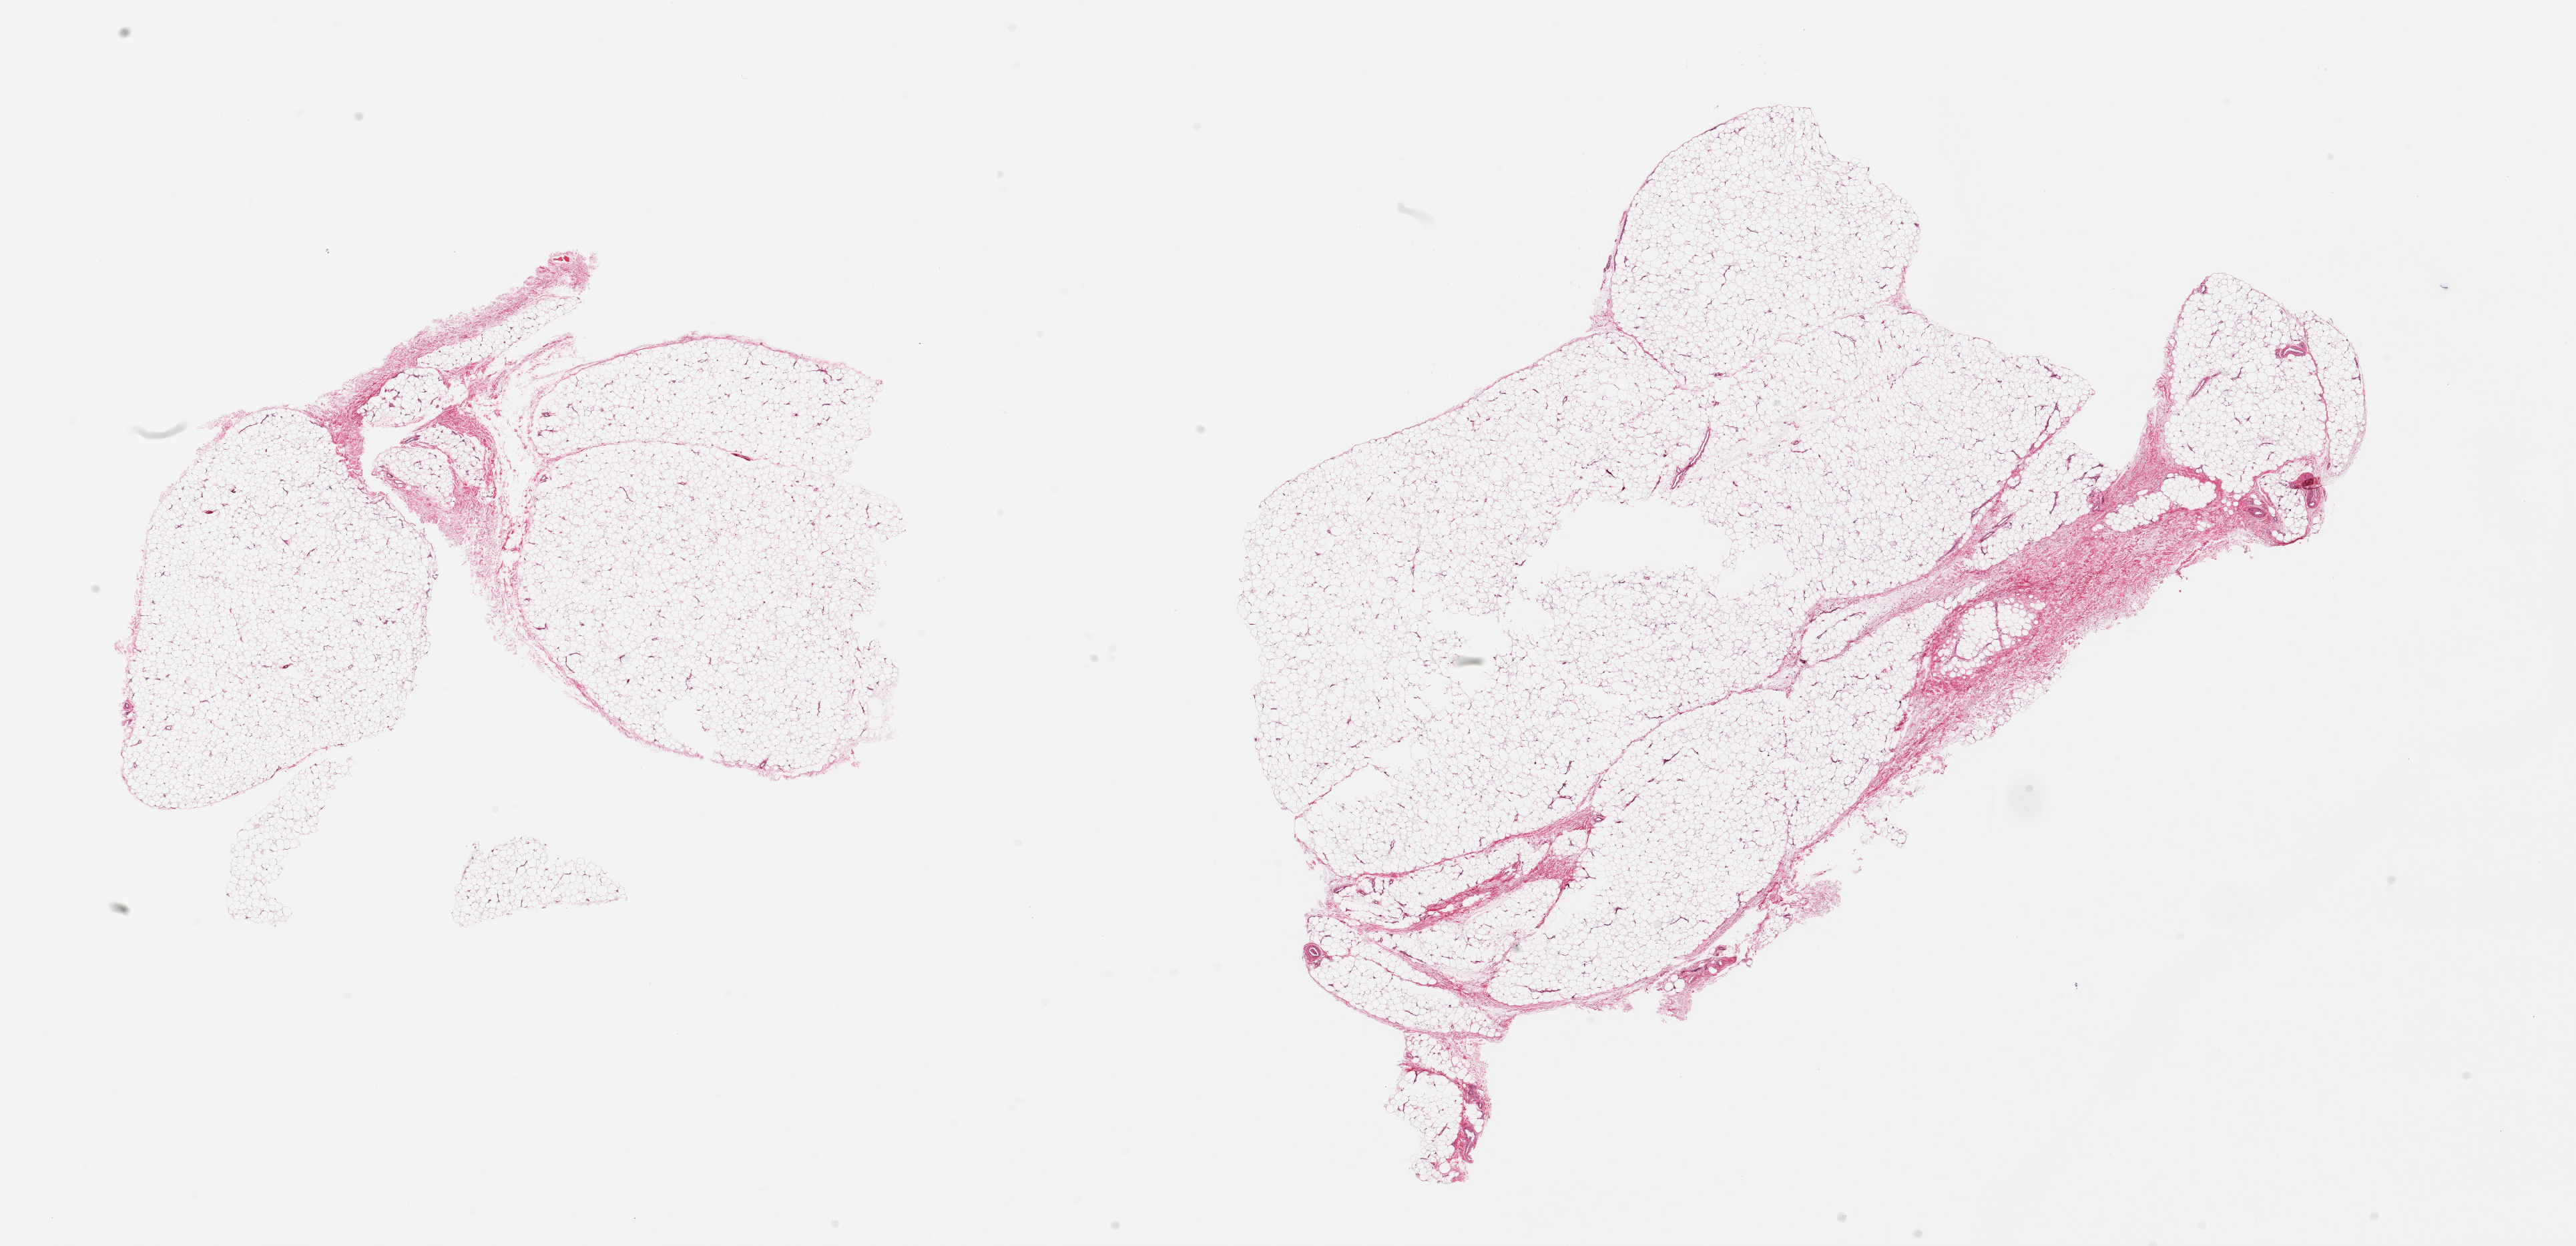
H&E whole-slide image, shown as a low-resolution overview of the whole scanned area (about 30.5 x 14.8 mm); PAXgene-fixed, paraffin-embedded tissue; section of adipose tissue (target tissue); donor tissue sample. Donor sex: male.
Reviewer comment on this tissue sample: 2 pieces; mature adipose tissue <10% fibrovascular tissue.